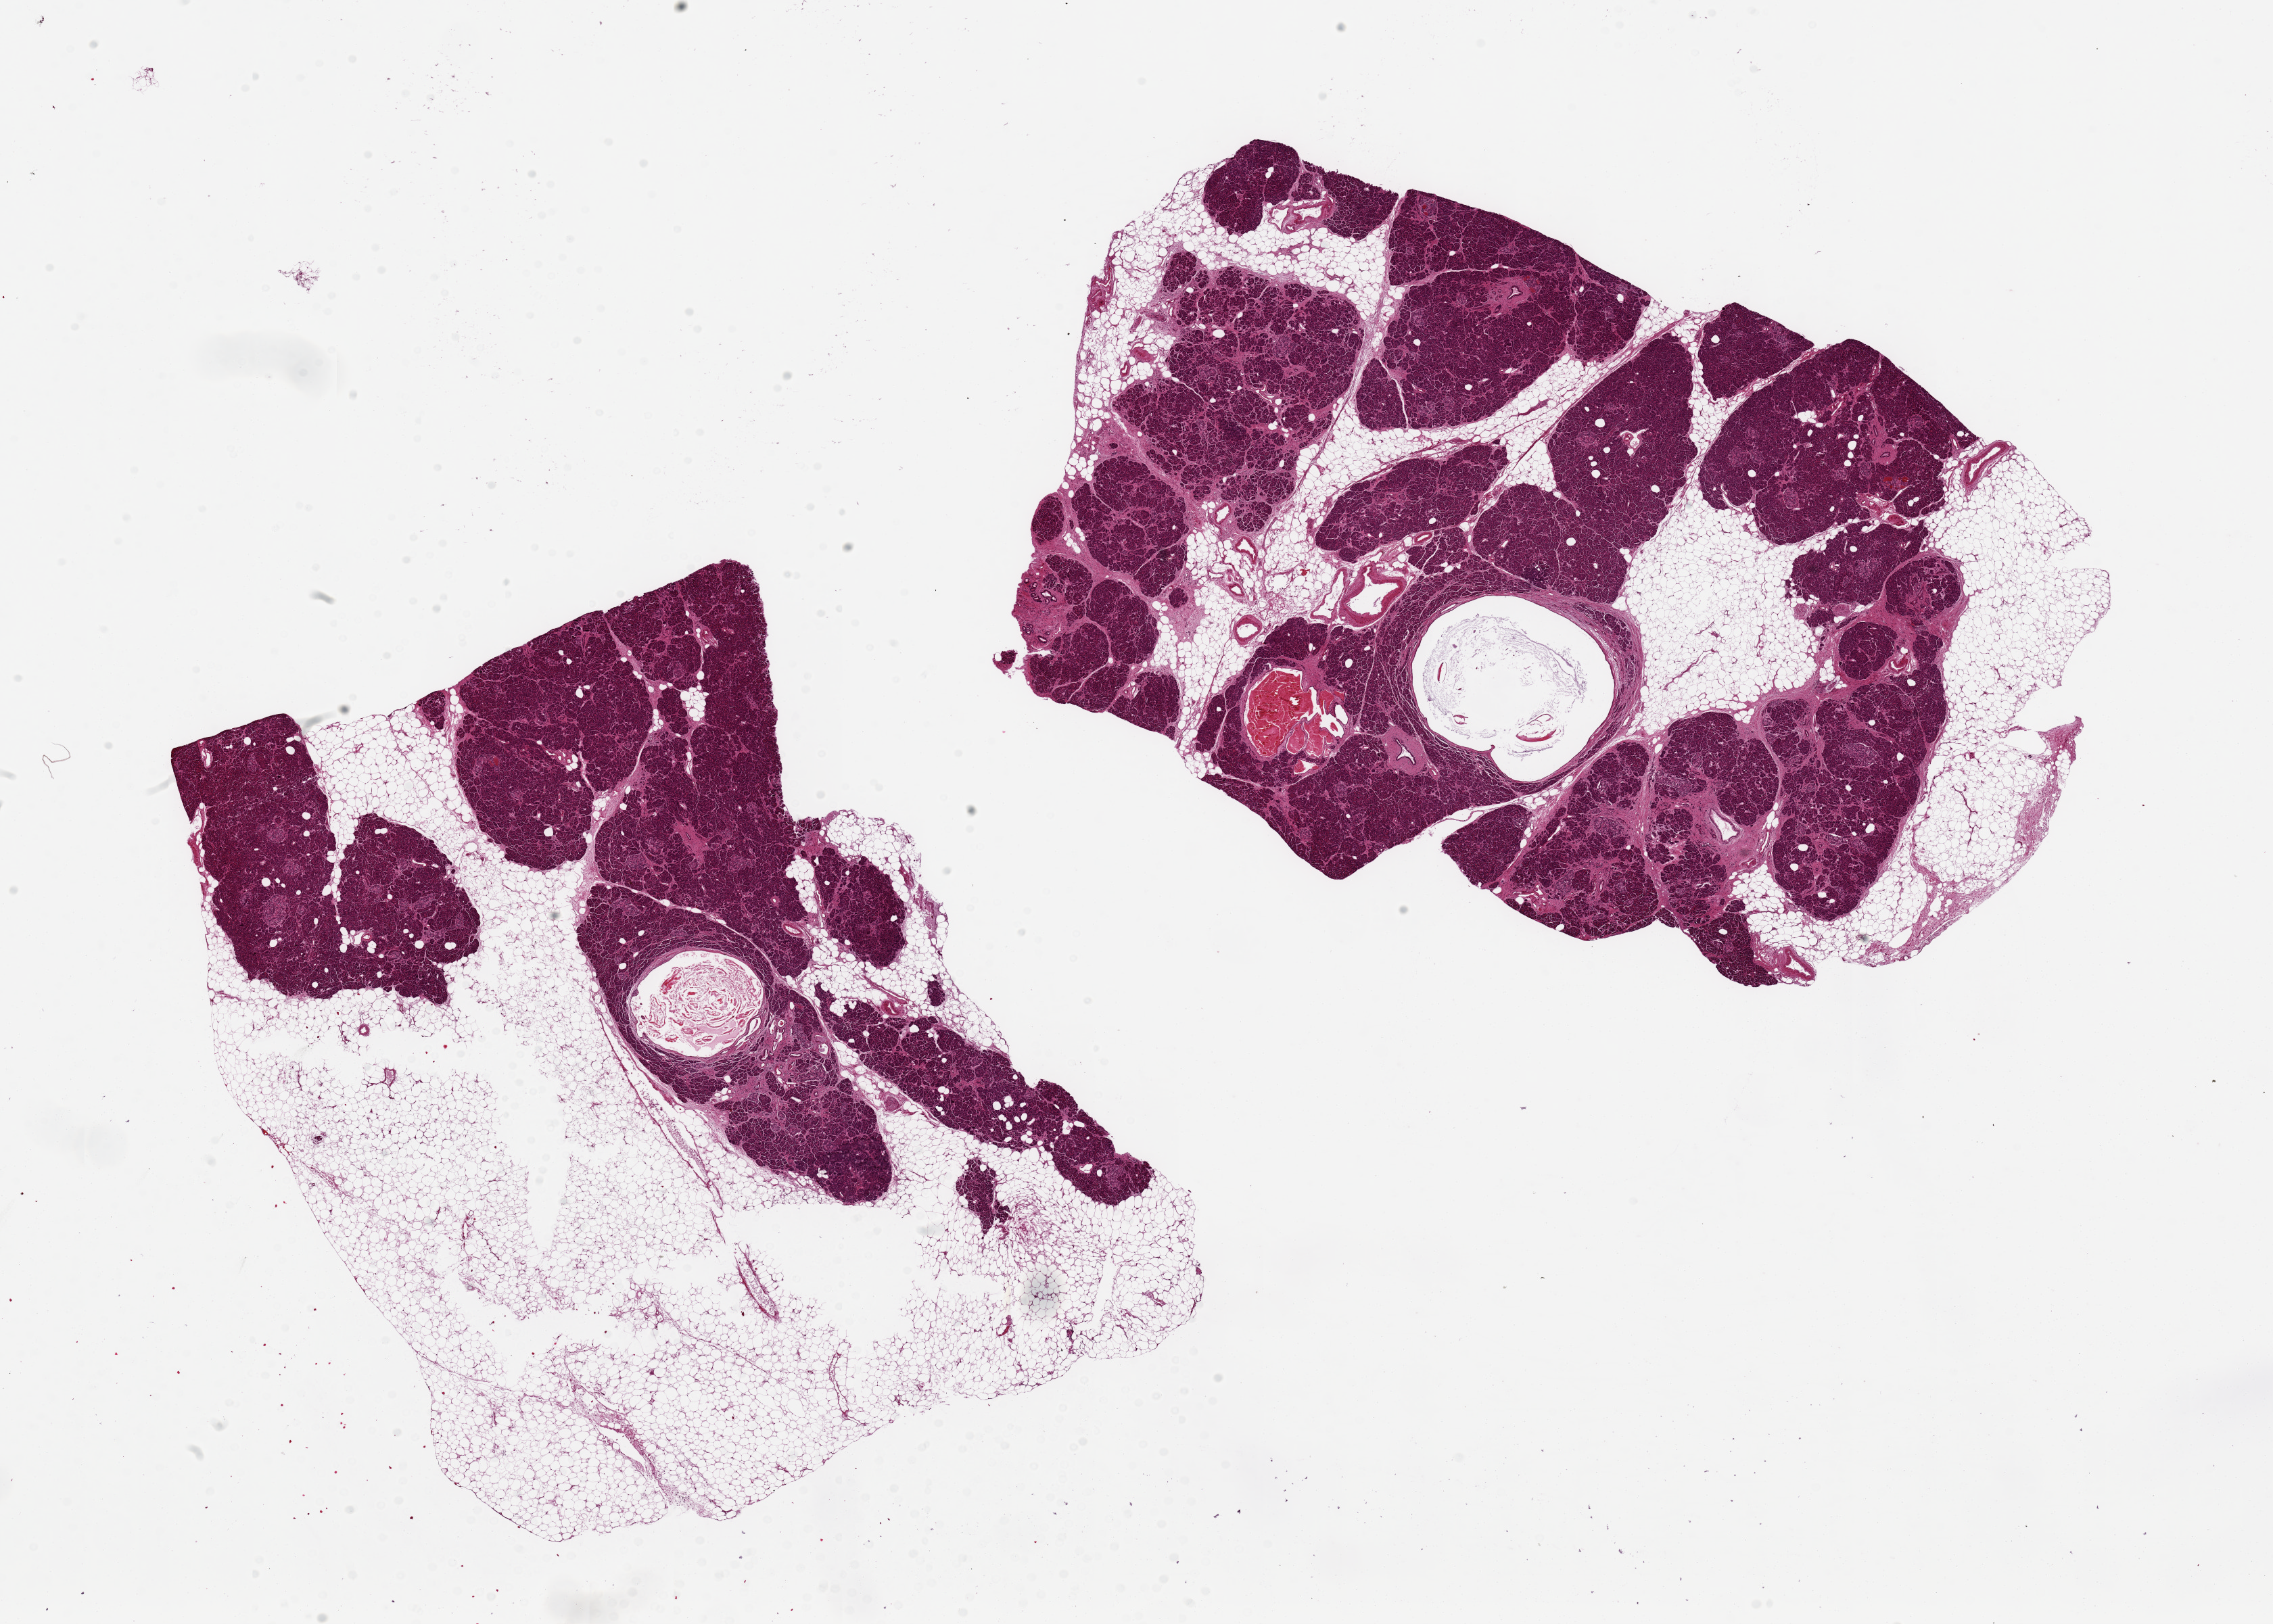
Digitized hematoxylin and eosin (H&E)-stained section, whole scanned area (about 26.6 x 19.0 mm, slide scanned at 20x) shown as a low-resolution overview; PAXgene-fixed, paraffin-embedded tissue; section of pancreas (target tissue); donor tissue sample. Donor: male.
Reviewer comment on this tissue sample: 2 pieces 12x6 & 10x7; two cysts up to 2 mm. patchy fibrosis; interna; and external adipose ~40%.